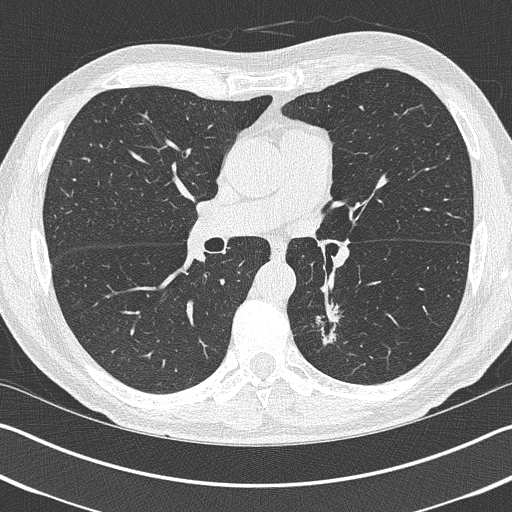
Axial slice from a low-dose chest CT screening exam, baseline screening round, lung window (W 1500 / L -600 HU), 1 mm slice thickness, slice 174 of 402 in the series. Male participant, aged 69 years at enrolment. Current smoker at enrolment.
• Expert-annotated lung lesion, bounding box [x1, y1, x2, y2] px = [295, 305, 352, 363].
• Reader record for this screening exam (exam-level; its link to the box is not recorded): non-calcified nodule or mass ≥4 mm, left upper lobe, 19 × 19 mm, spiculated (stellate) margins, pre-existing on the prior screen: yes.
• Official screen result: positive, change unspecified: nodule(s) >= 4 mm or enlarging nodule(s), mass(es), or other non-specific abnormalities suspicious for lung cancer.
• Later outcome: lung cancer diagnosed 202 days after this screen — non-small cell carcinoma, left lower lobe, stage IIIA (AJCC 6th edition), 20 mm at pathology.